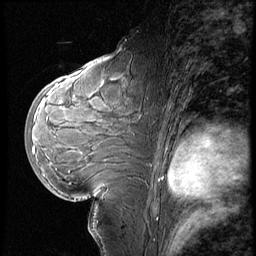
Breast MRI (dynamic contrast-enhanced), one sagittal slice; 3 images stored at this slice position (order not interpretable as contrast timing); 1.5 T; TE 4.2 ms, TR 8.9 ms; 2.5 mm slice thickness; 256 × 256 image matrix, field of view 200 × 200 mm. Female patient, age 29 years. From the clinical record (not read from this slice): setting: breast cancer imaged before/during neoadjuvant chemotherapy.
Annotated regions visible in this slice (semi-automatic segmentation, software-assisted and operator-edited):
- analysis volume of interest (the breast-tissue region the enhancement analysis was run in; not a lesion): box from (x=29, y=57) to (x=150, y=200) px
- tumour enhancement mask (voxels above the 140 % enhancement threshold inside the analysis volume of interest): (x=34, y=86)–(x=60, y=154)